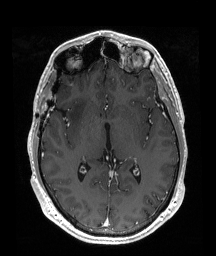
Brain MRI from a brain-tumour surgery series, one axial slice; position 105 of 192 along the scan axis; T1-weighted post-contrast; 216 × 256 image matrix, field of view 219 × 260 mm. From the clinical record (not read from this slice): histopathology: Astrocytoma; WHO grade: 2; IDH mutation: yes.
Outlined on this slice (expert manual segmentation):
- tumour: bounding box (x1, y1, x2, y2) in pixels: (69, 94, 91, 130)